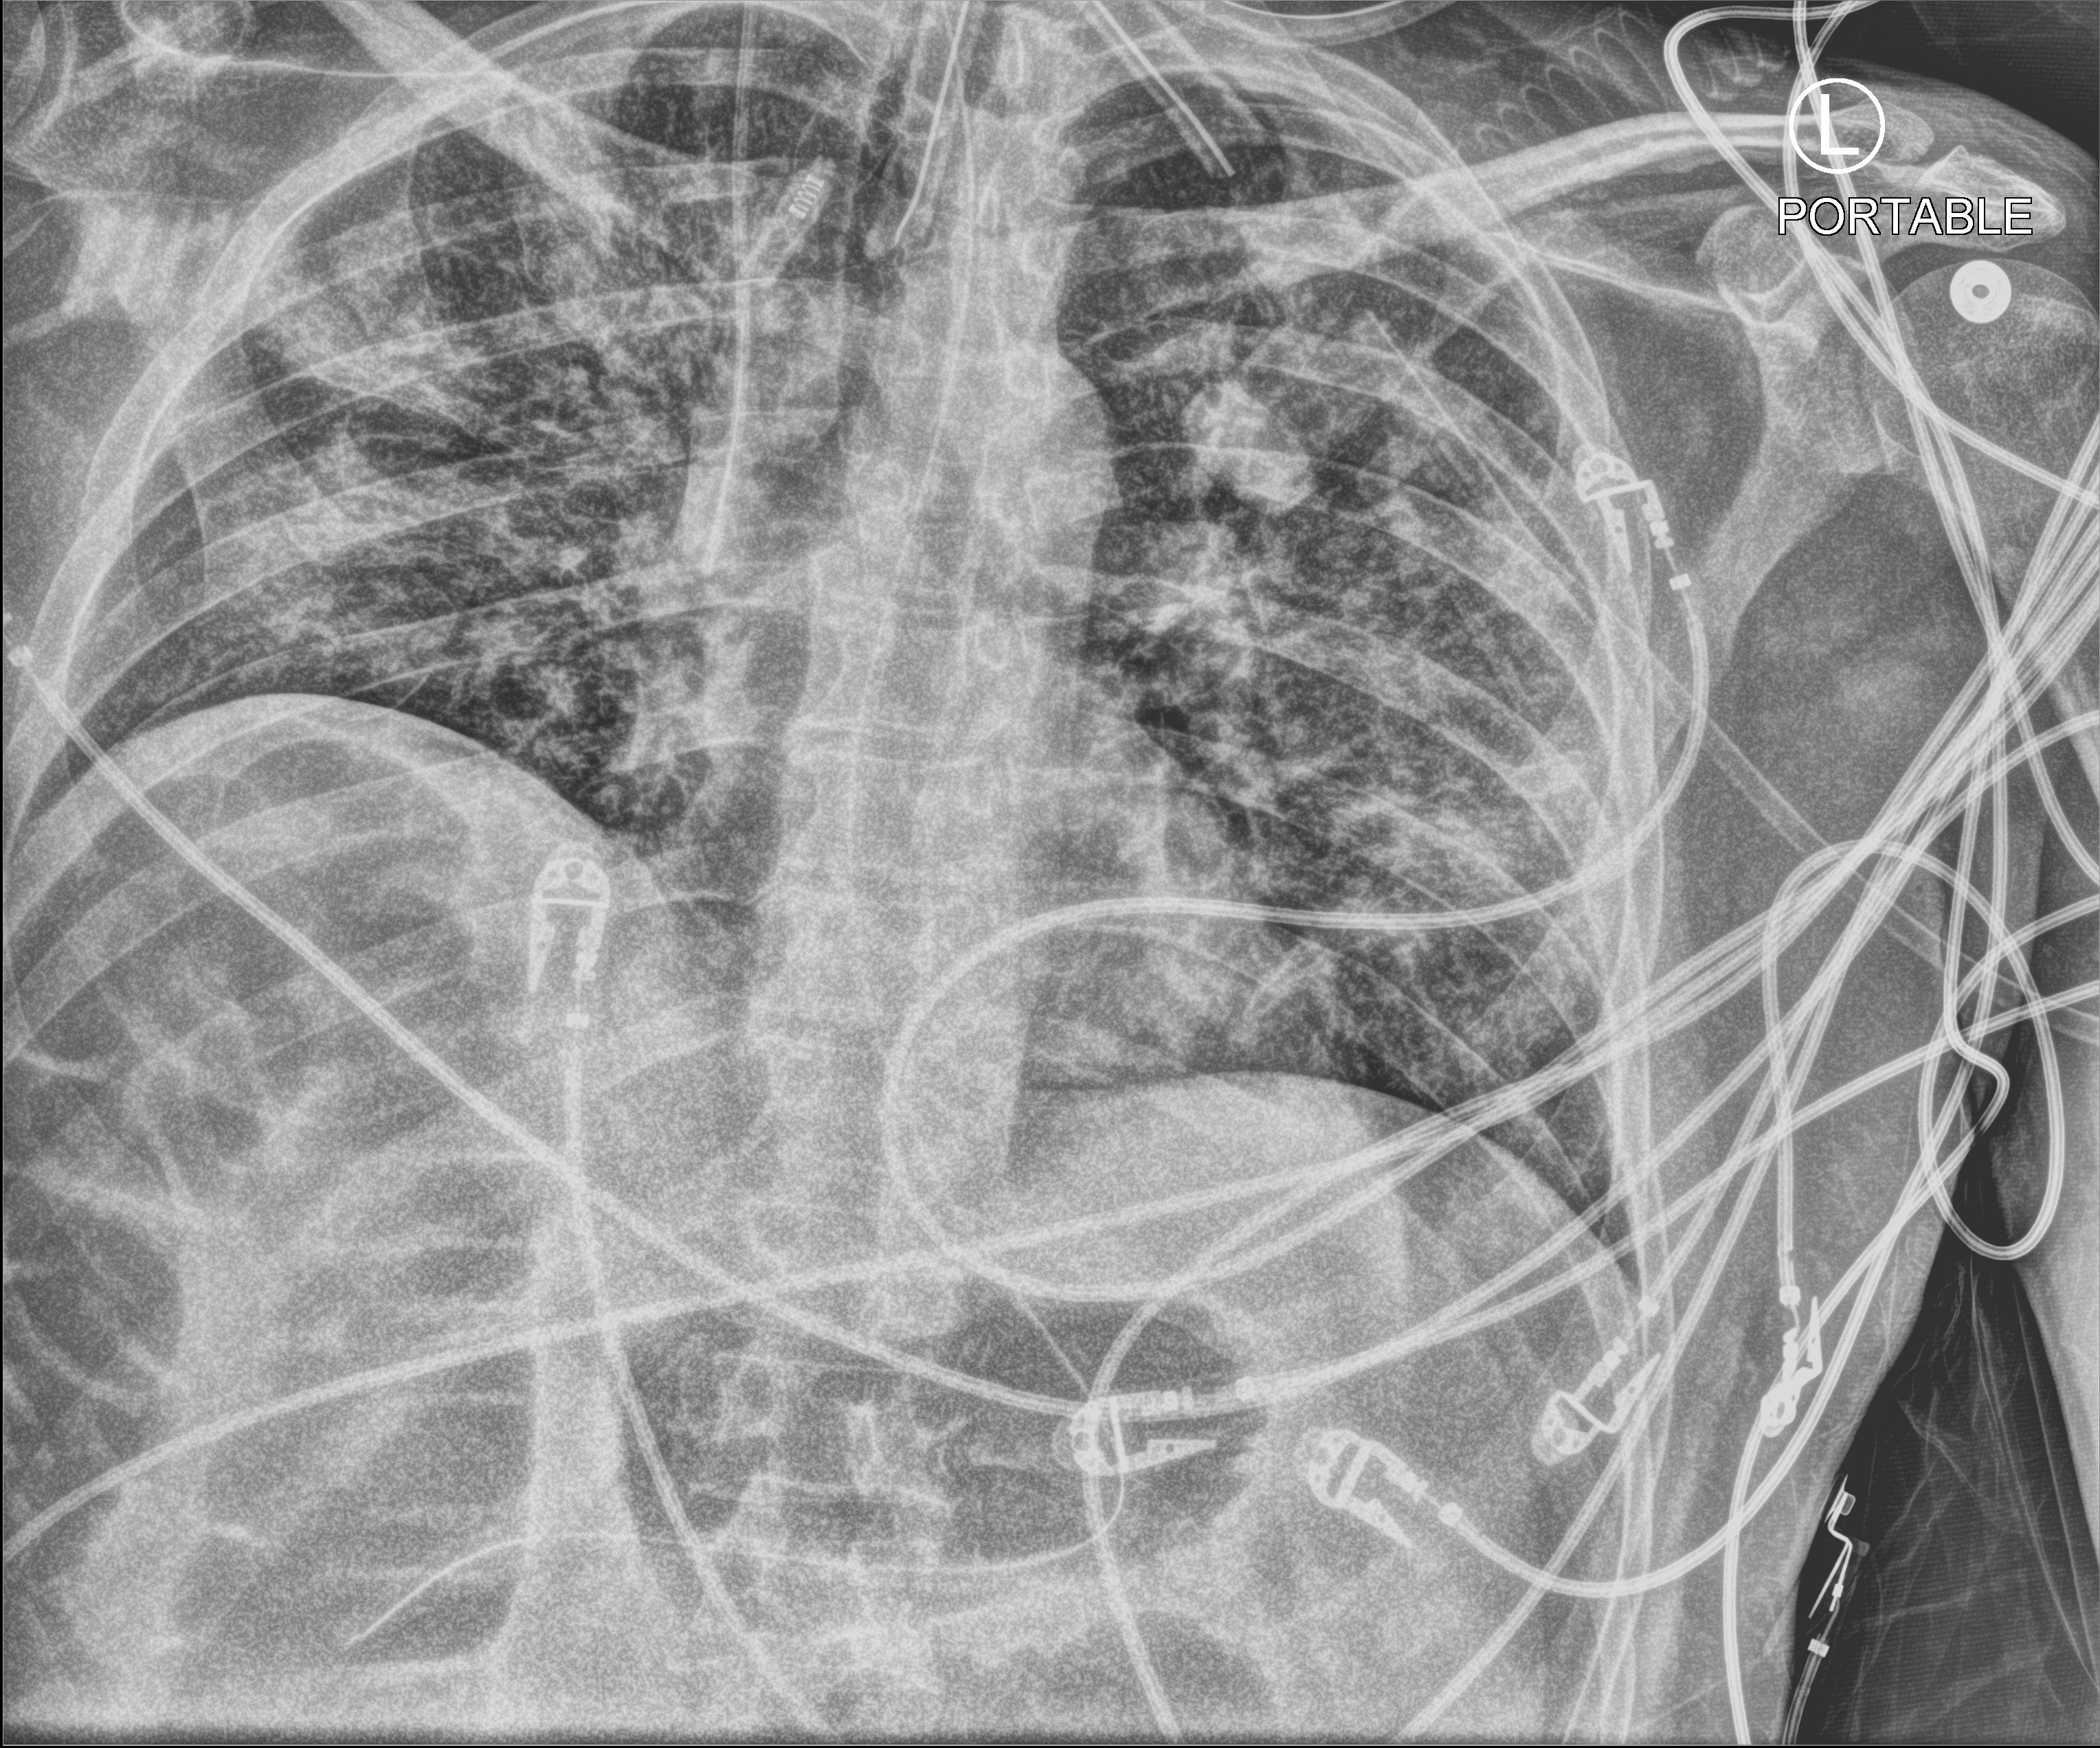
Chest X-ray (portable), anteroposterior (AP) projection. Male patient hospitalised with COVID-19, age 18–59 years.
Hospital-stay facts (about this admission, not read from this image; timing relative to this image not recorded): diabetes (admission record): no.